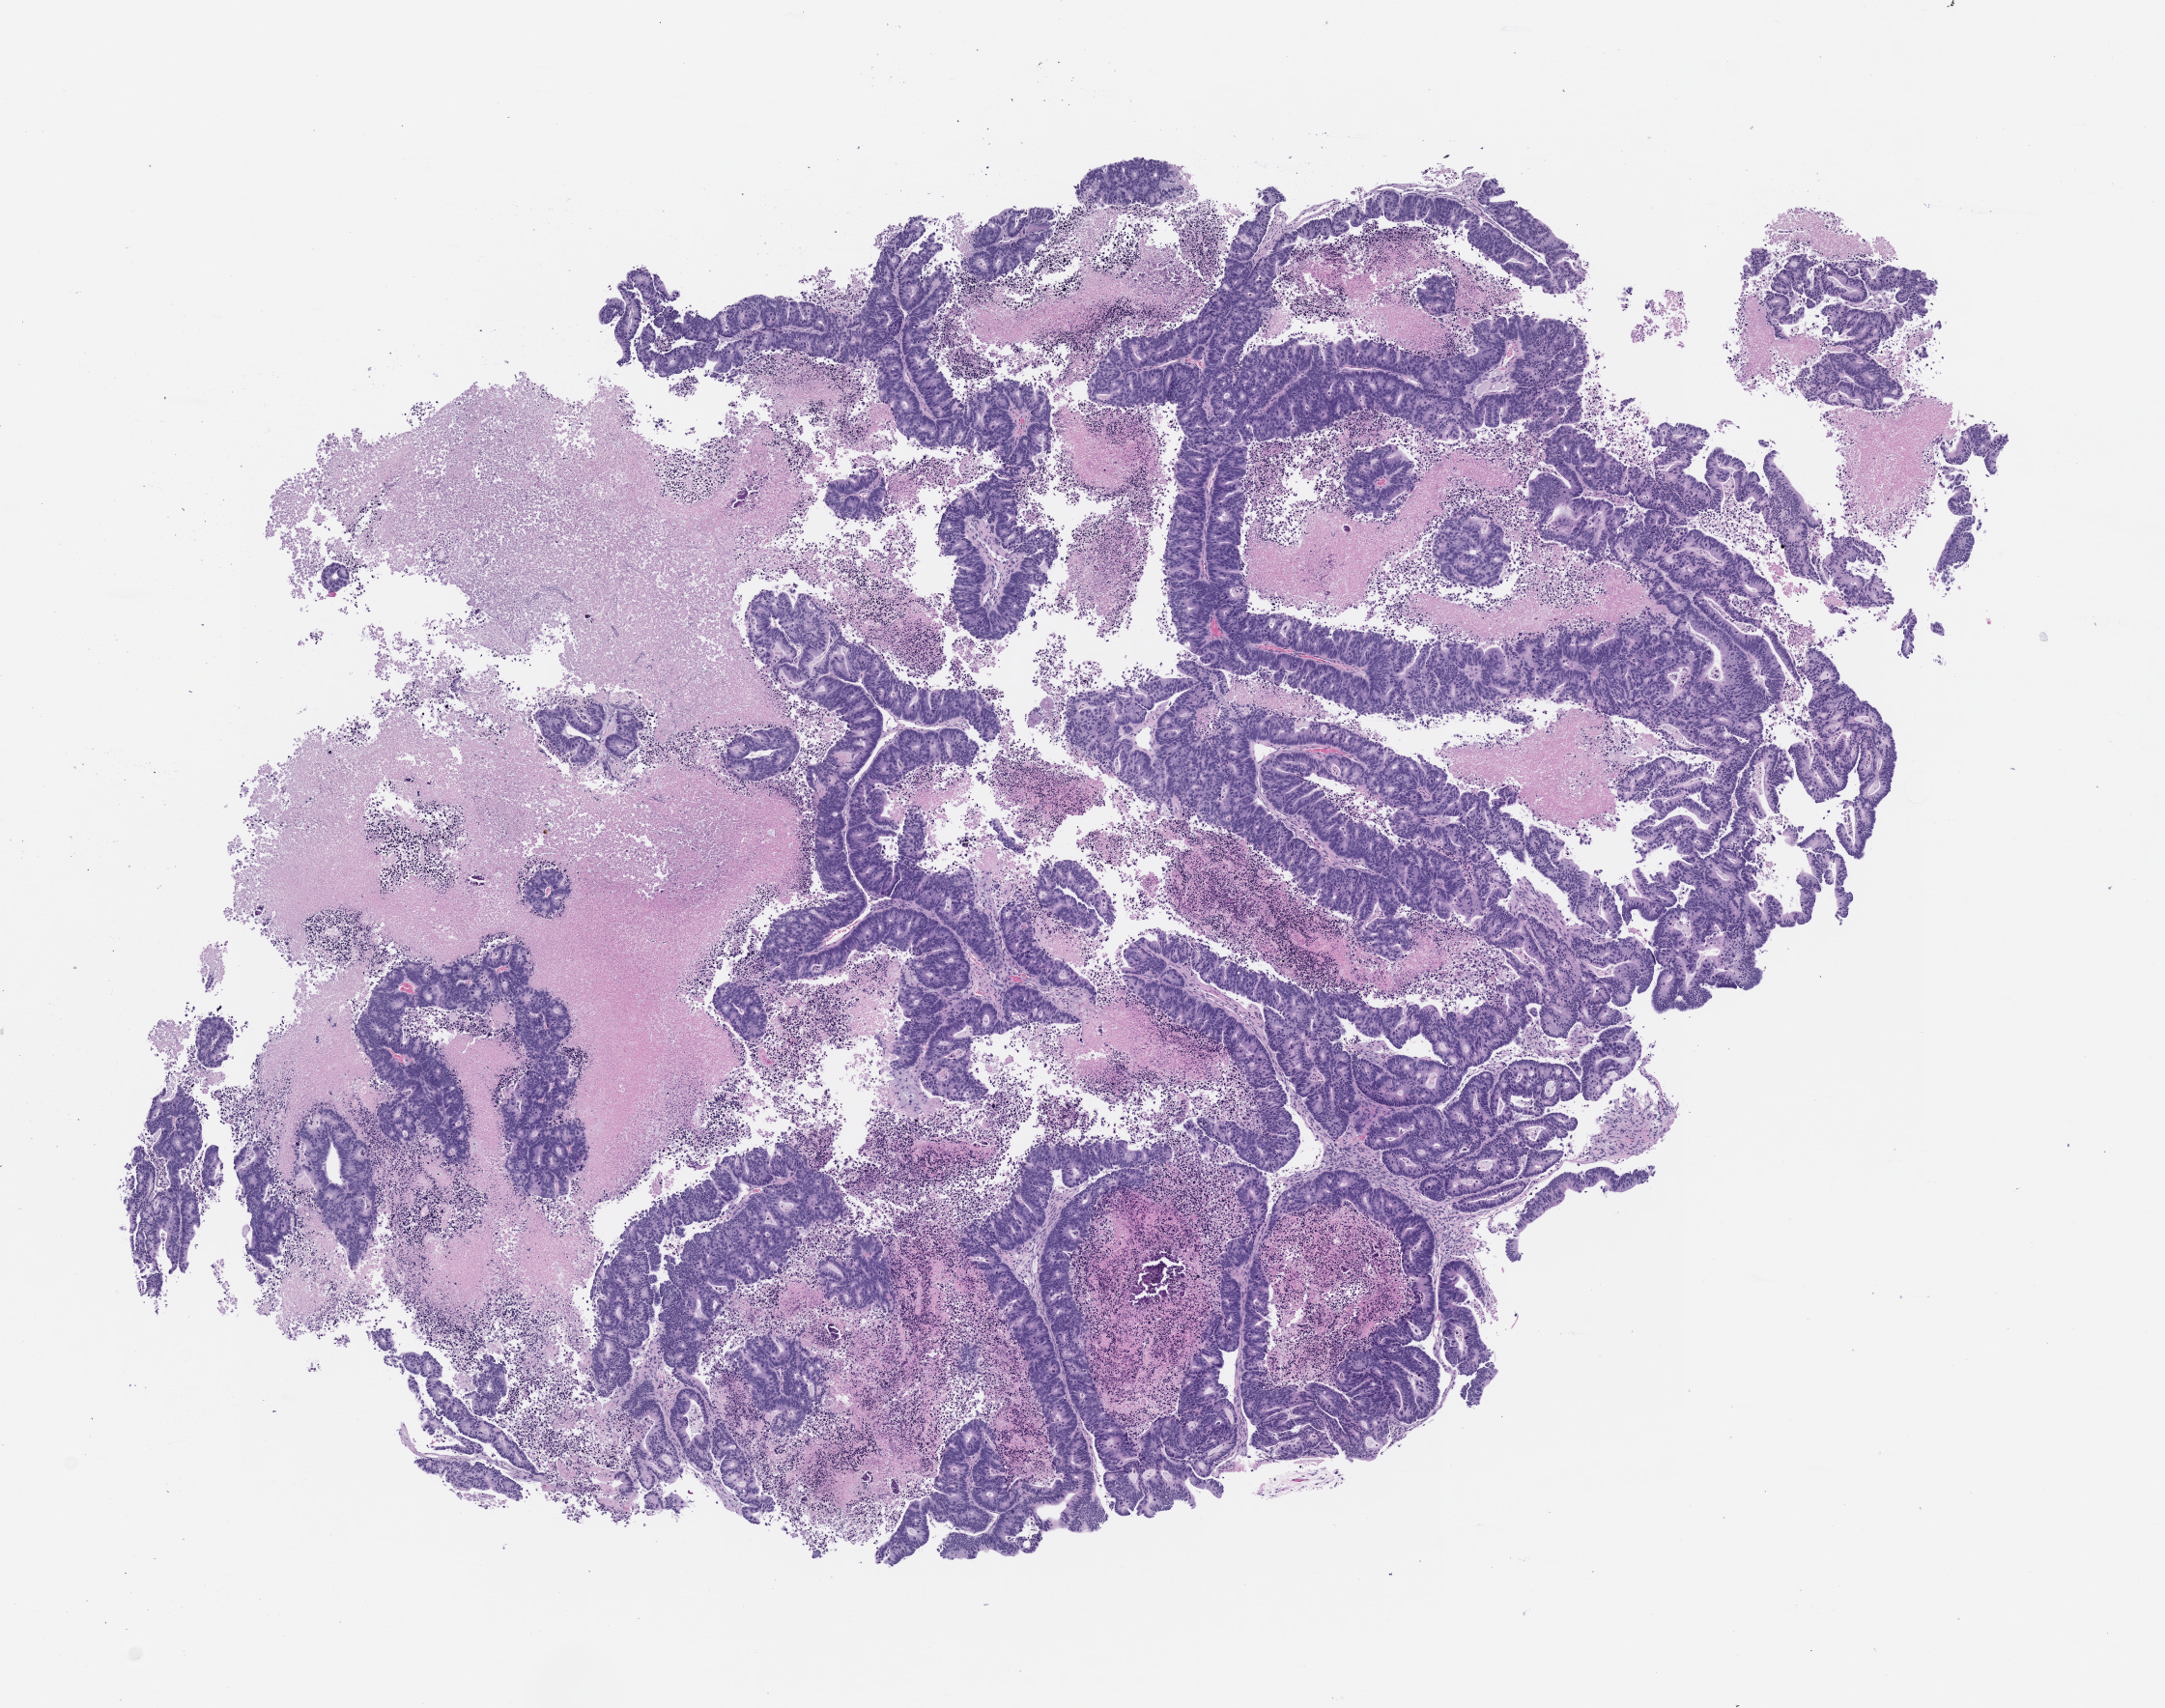
Haematoxylin and eosin whole-slide image of a patient-derived xenograft (PDX) tumor grown in a mouse, passage 1 — low-resolution overview of the scanned area, about 9.0 x 7.1 mm, formalin-fixed, paraffin-embedded (FFPE) tissue, originating tumor site category: colon.
Originating patient diagnosis: Colon Adenocarcinoma.